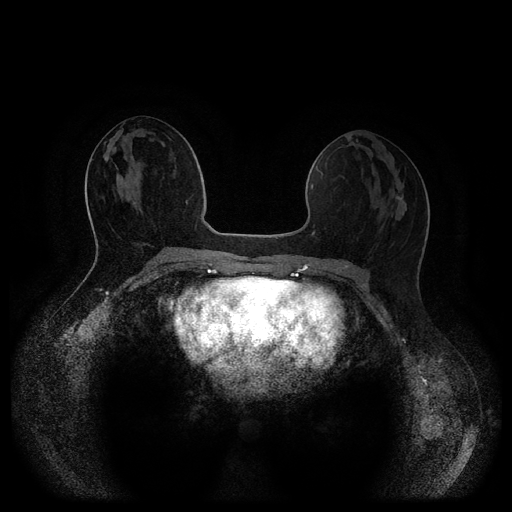
Breast MRI (dynamic contrast-enhanced, multi-phase), one axial slice. Slice 48 of 116 in the series (ordered by position). Dynamic contrast-enhanced series, time point 2 of 5 at this slice position (early post-contrast). 1.5 T. TE 2.6 ms, TR 5.3 ms. 2 mm slice thickness. 512 × 512 image matrix, field of view 360 × 360 mm. Patient: female, 27 years.
Annotated regions visible in this slice (semi-automatically segmented with operator editing):
- breast lesion (labelled 'tumour' in the annotation; benign lesions carry a separate 'benign' label): bounding box (x1, y1, x2, y2) in pixels: (396, 184, 404, 201)